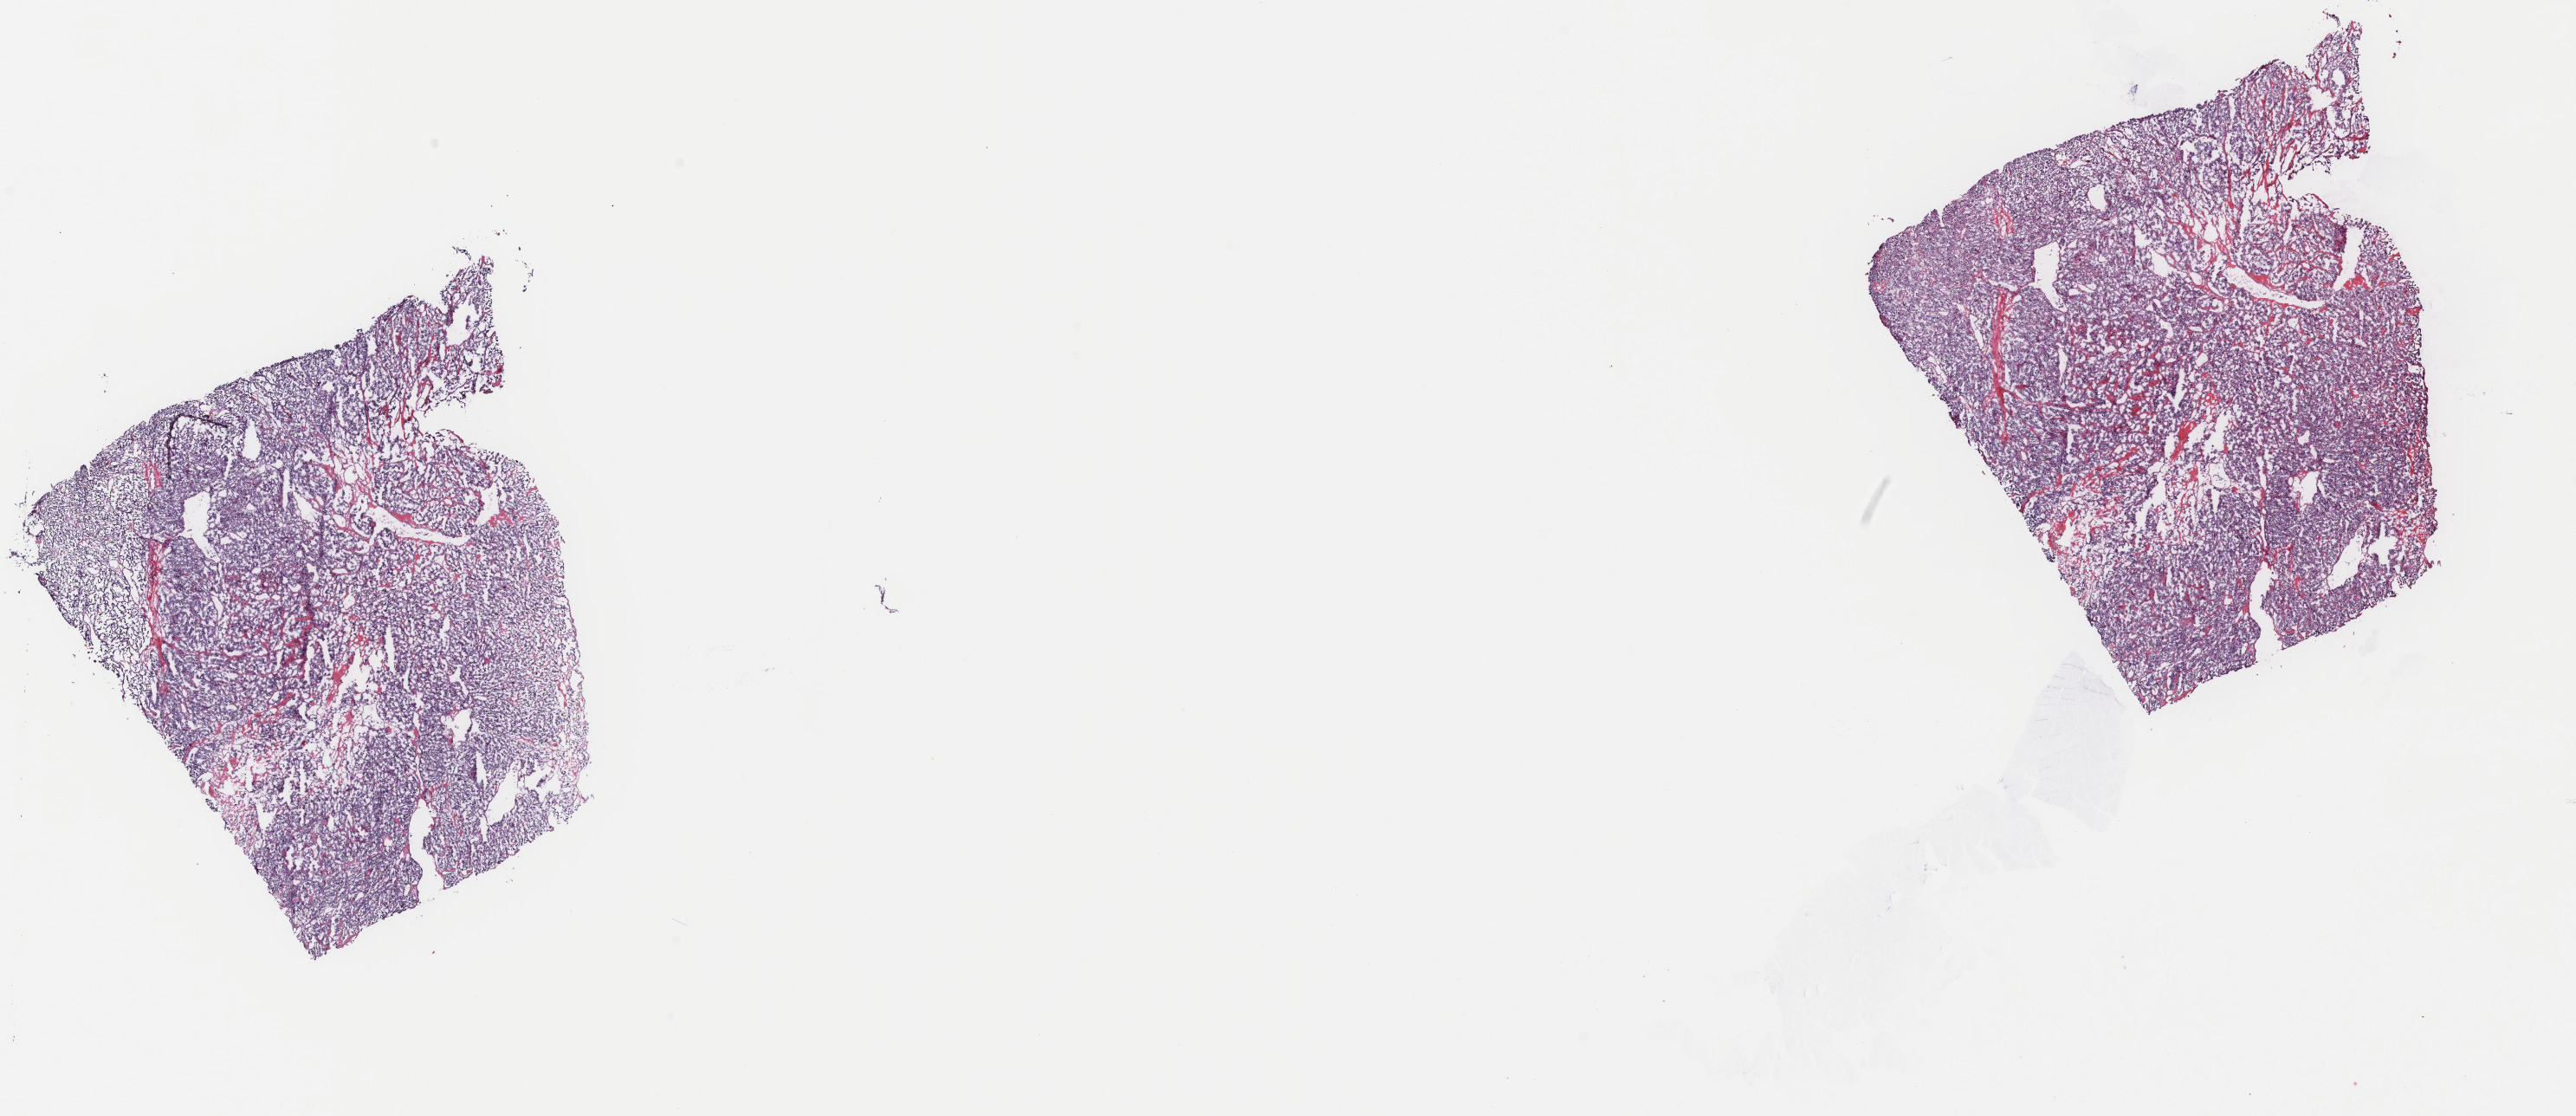
Whole-slide histology image, H&E — shown as a low-resolution overview of the whole scanned area (about 23.6 x 10.2 mm). Frozen section. Sample: primary tumour, heart, mediastinum, and pleura. Female, age 63 years at initial diagnosis. Slide review estimates, as recorded: tumour cells 90%, tumour nuclei 90%, normal cells 0%, stromal cells 10%, necrosis 0%. Infiltration values recorded for this section: lymphocyte infiltration 0%, monocyte infiltration 0%, neutrophil infiltration 0%.
• diagnosis: Extra-adrenal paraganglioma, NOS (heart)
• lymph nodes positive (case pathology): 0 of 3 examined